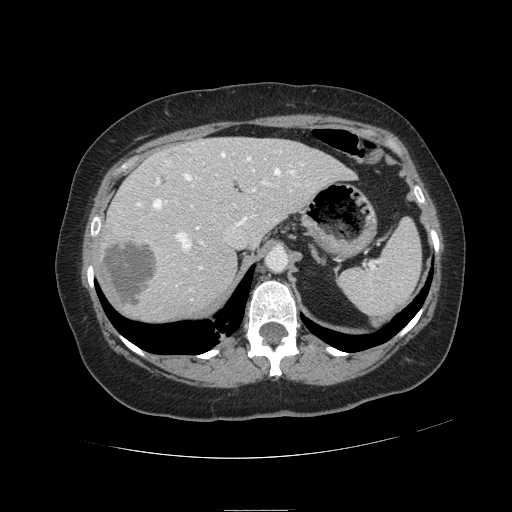
Contrast-enhanced abdominal CT, one axial slice. Slice 81 of 121 in the series (ordered by position). 120 kVp. Intravenous contrast given. Soft-tissue window (W 400 / L 40 HU). 2.5 mm slice thickness. 512 × 512 image matrix, field of view 400 × 400 mm. Female patient, age 52 years. Case-level facts recorded for this patient, not image findings: diagnosis: colorectal cancer liver metastases, imaged before liver resection; multiple liver metastases: yes; largest metastasis: 6.3 cm; disease in both lobes: no.
Structures marked on this image (expert manual segmentation):
- hepatic veins: bounding box <136,151,303,249> (left, top, right, bottom; pixels)
- liver: <100,137,351,320>
- planned liver remnant (the part of the liver to remain after resection): <168,137,351,243>
- portal vein (with intrahepatic branches): <156,158,270,291>
- liver metastasis: <103,240,158,306>